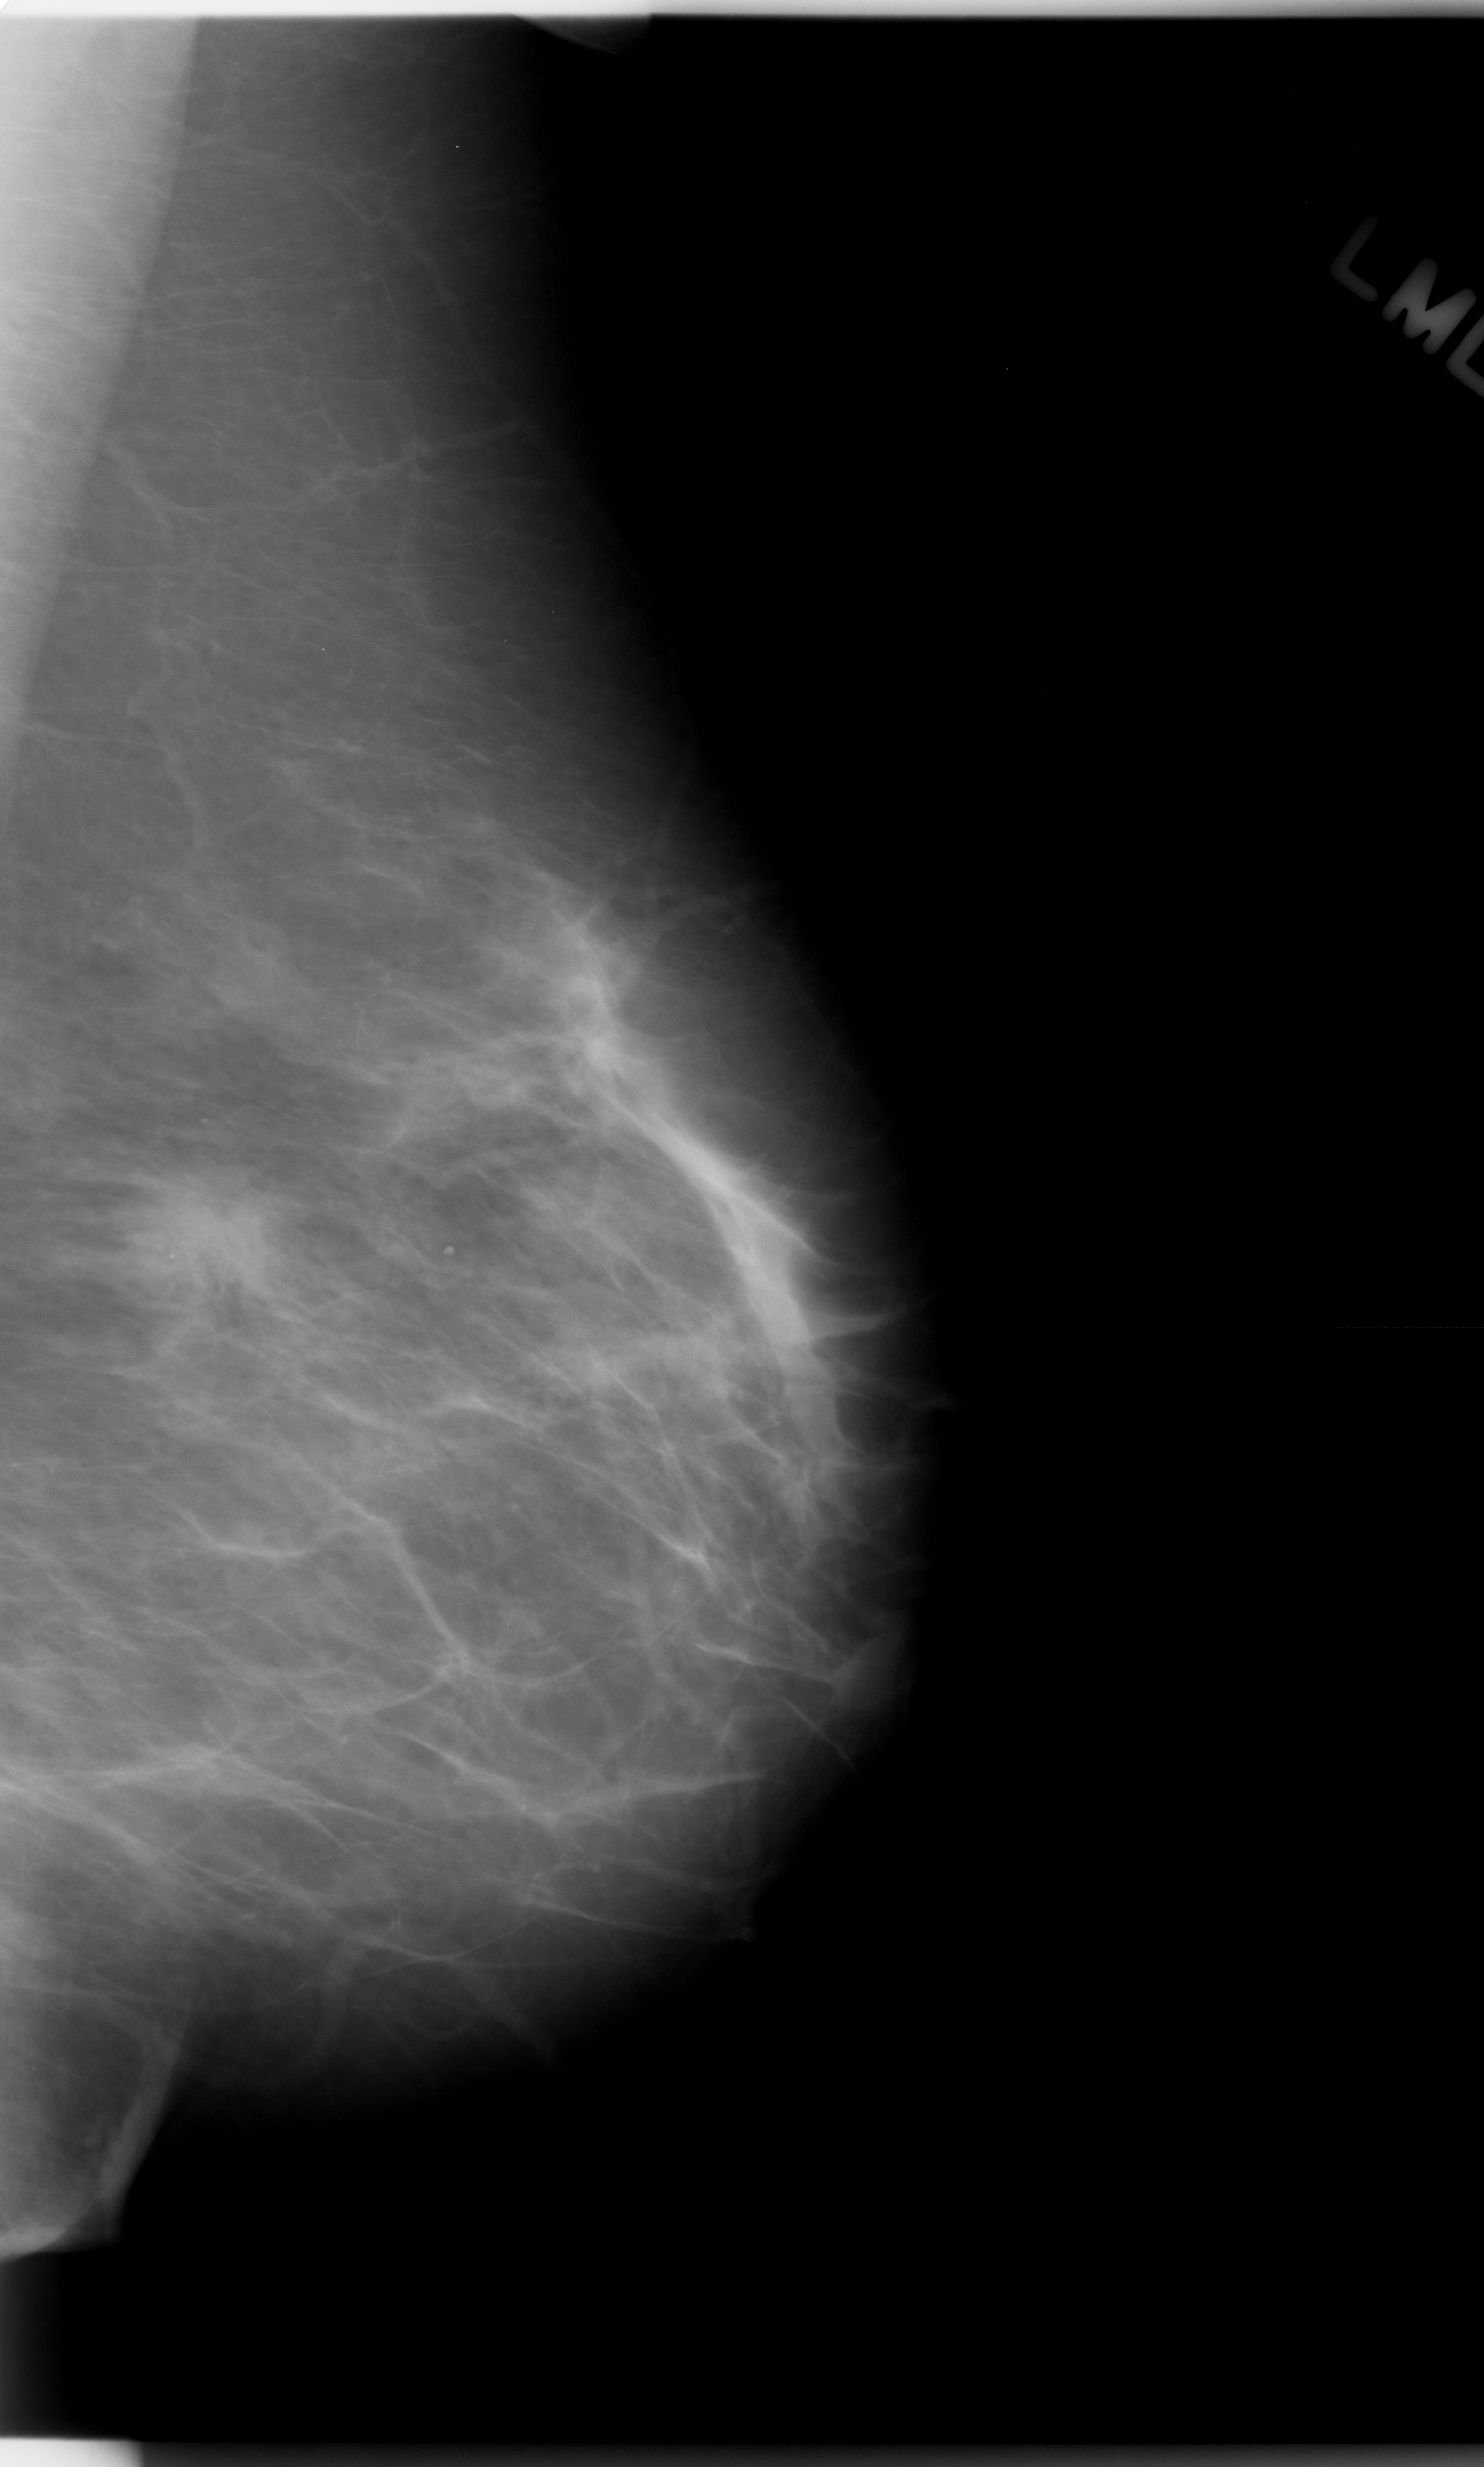
Scanned film-screen mammogram; left breast; MLO view; 1484 × 2467 image matrix.
Expert-marked regions of interest on this film, with their recorded descriptors:
- mass, shape irregular, margins spiculated; BI-RADS assessment category 5; subtlety rating 5 on a 1 (subtle) to 5 (obvious) scale; pathology (as recorded): malignant: box from (x=108, y=1158) to (x=304, y=1356) px